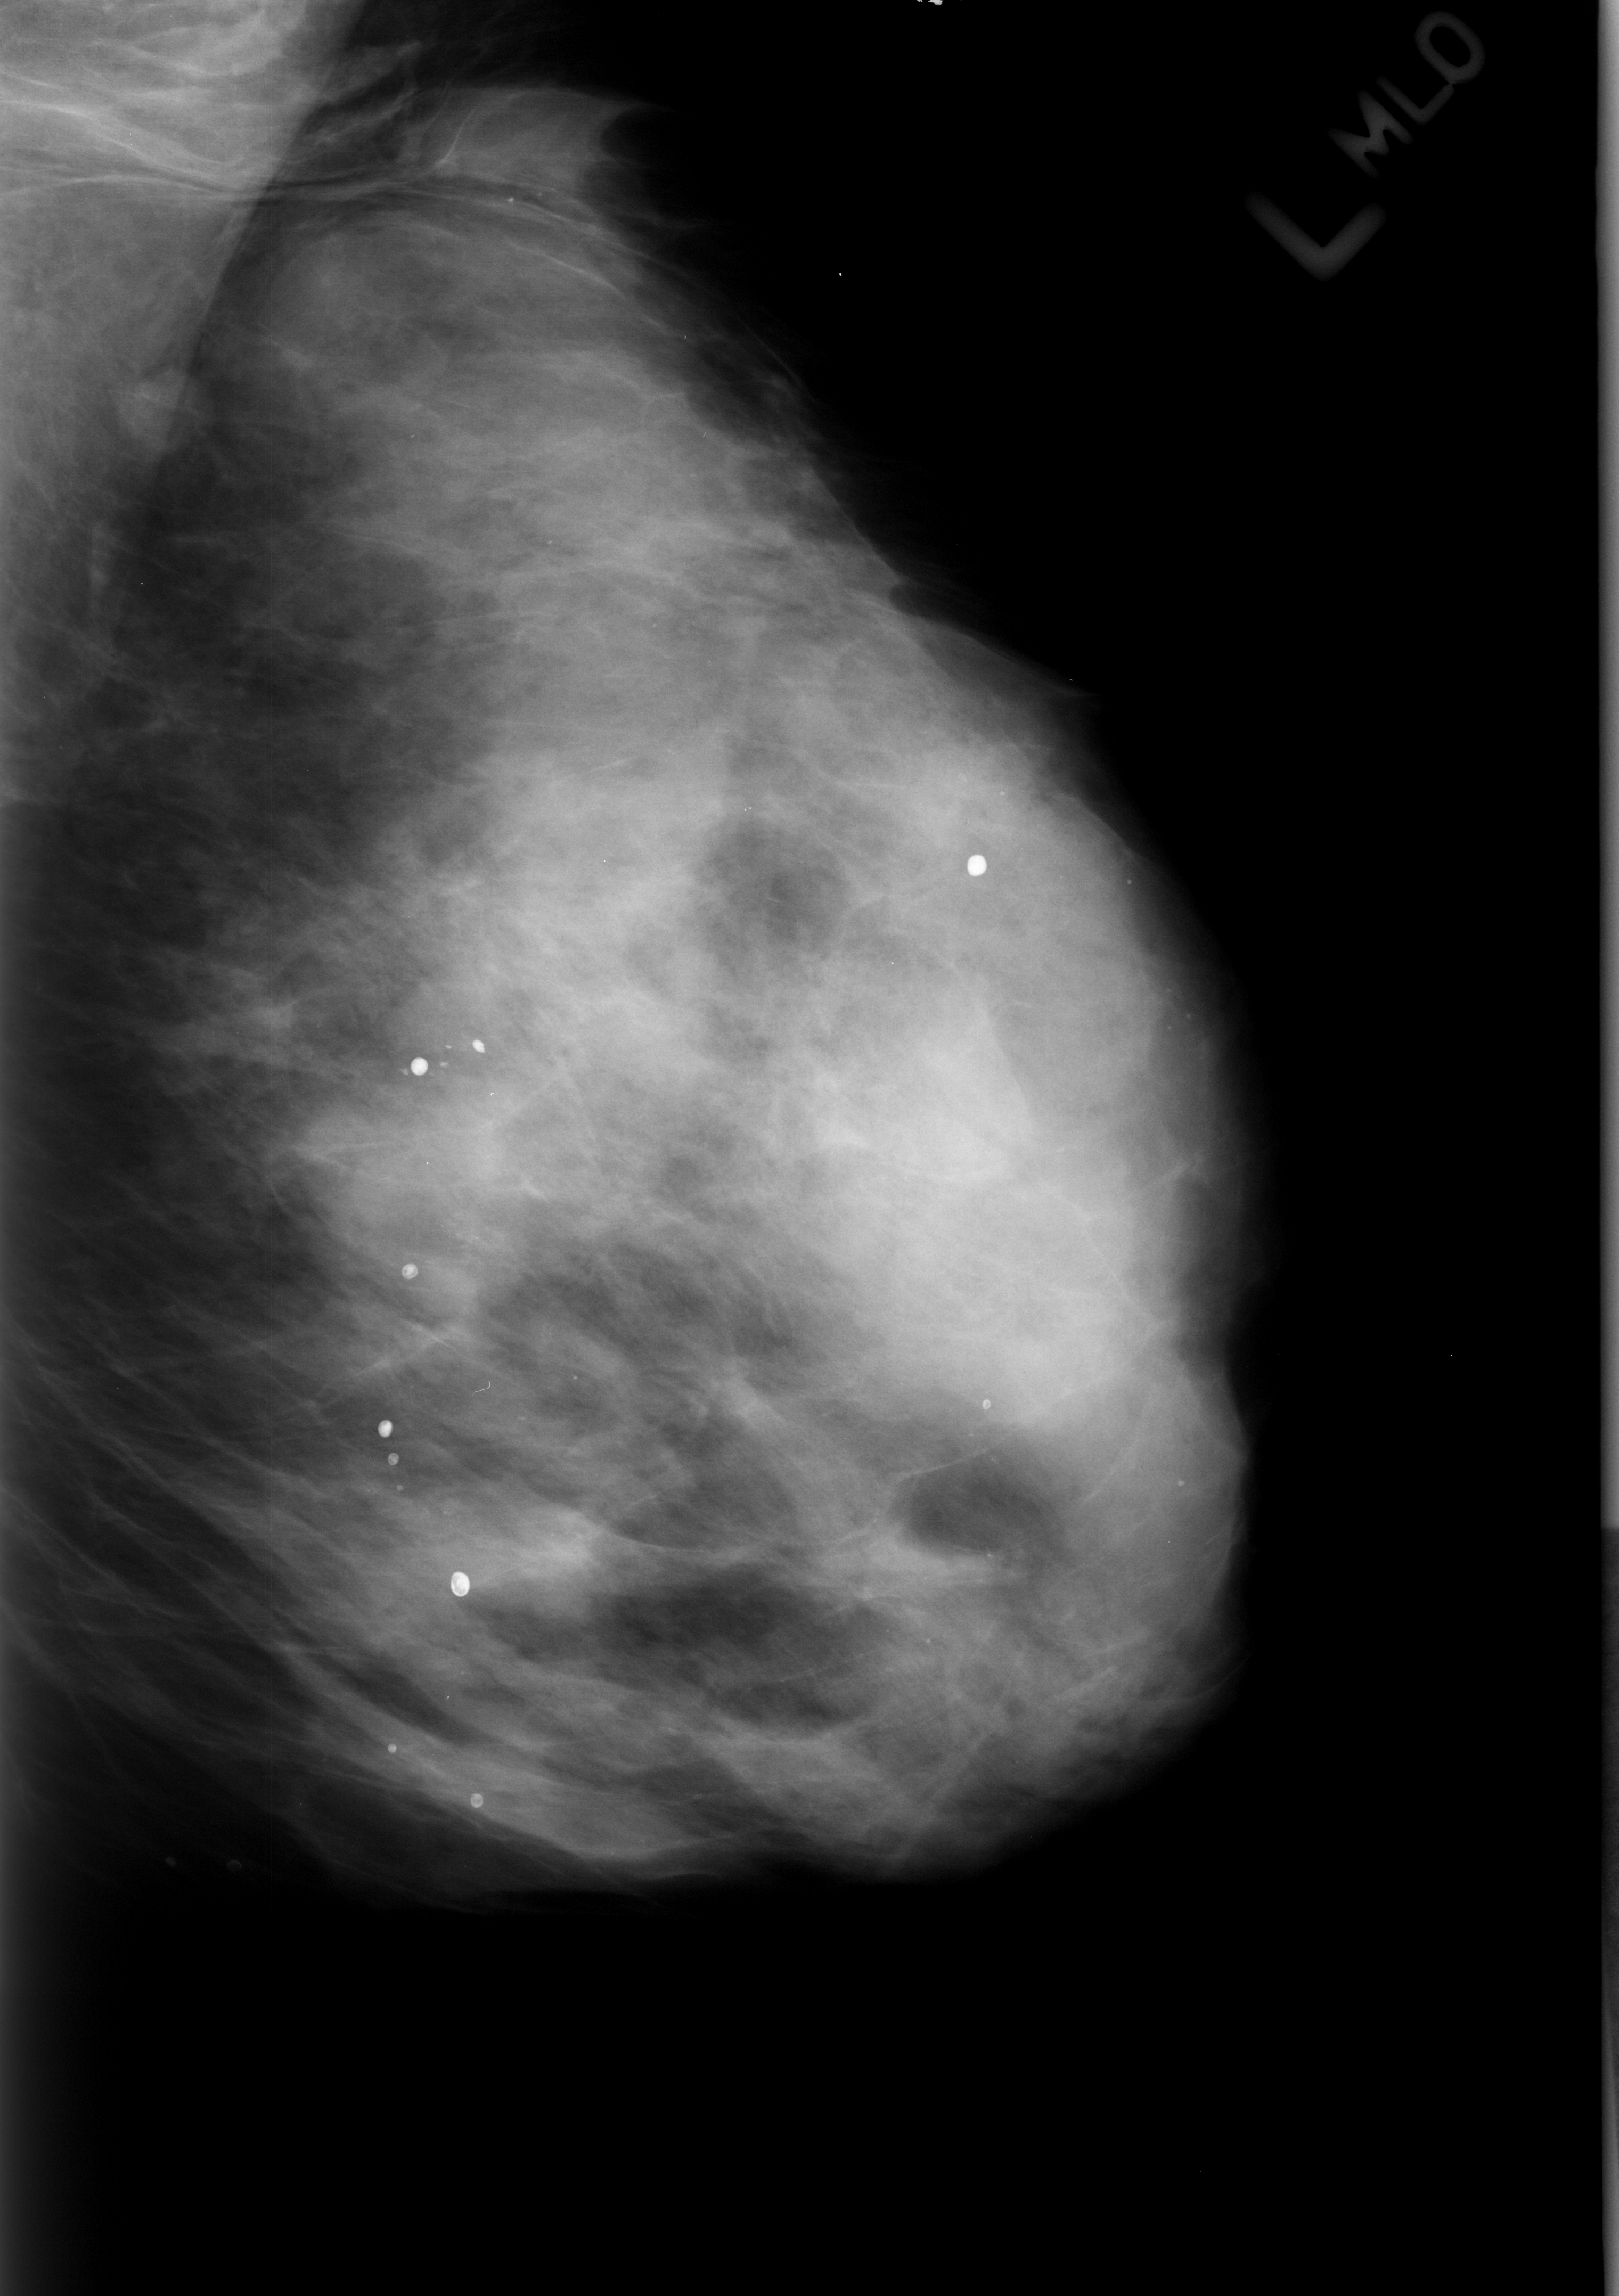
Mammogram (digitized film), left breast, MLO view, breast composition: extremely dense (BI-RADS density category 4 of 4).
Marked findings (only marked abnormalities are described; nothing is implied about the rest of the image): Finding 1 of 6: calcifications, morphology round and regular / lucent center / punctate, distribution diffusely scattered; BI-RADS assessment category 2; subtlety rating 5 on a 1 (subtle) to 5 (obvious) scale; benign without callback (not worked up further). Finding 2 of 6: calcifications, morphology round and regular / lucent center / punctate, distribution diffusely scattered; BI-RADS assessment category 2; subtlety rating 5 on a 1 (subtle) to 5 (obvious) scale; benign; no additional work-up was recommended (benign without callback). Finding 3 of 6: calcifications, morphology round and regular / lucent center / punctate, distribution diffusely scattered; BI-RADS assessment category 2; subtlety rating 5 on a 1 (subtle) to 5 (obvious) scale; benign; no additional work-up was recommended (benign without callback). Finding 4 of 6: calcifications, morphology round and regular / lucent center / punctate, distribution diffusely scattered; BI-RADS assessment category 2; subtlety rating 5 on a 1 (subtle) to 5 (obvious) scale; benign without callback (not worked up further). Finding 5 of 6: calcifications, morphology round and regular / lucent center / punctate, distribution diffusely scattered; BI-RADS assessment category 2; subtlety rating 5 on a 1 (subtle) to 5 (obvious) scale; benign; no additional work-up was recommended (benign without callback). Finding 6 of 6: calcifications, morphology round and regular / lucent center / punctate, distribution diffusely scattered; BI-RADS assessment category 2; benign without callback (not worked up further).